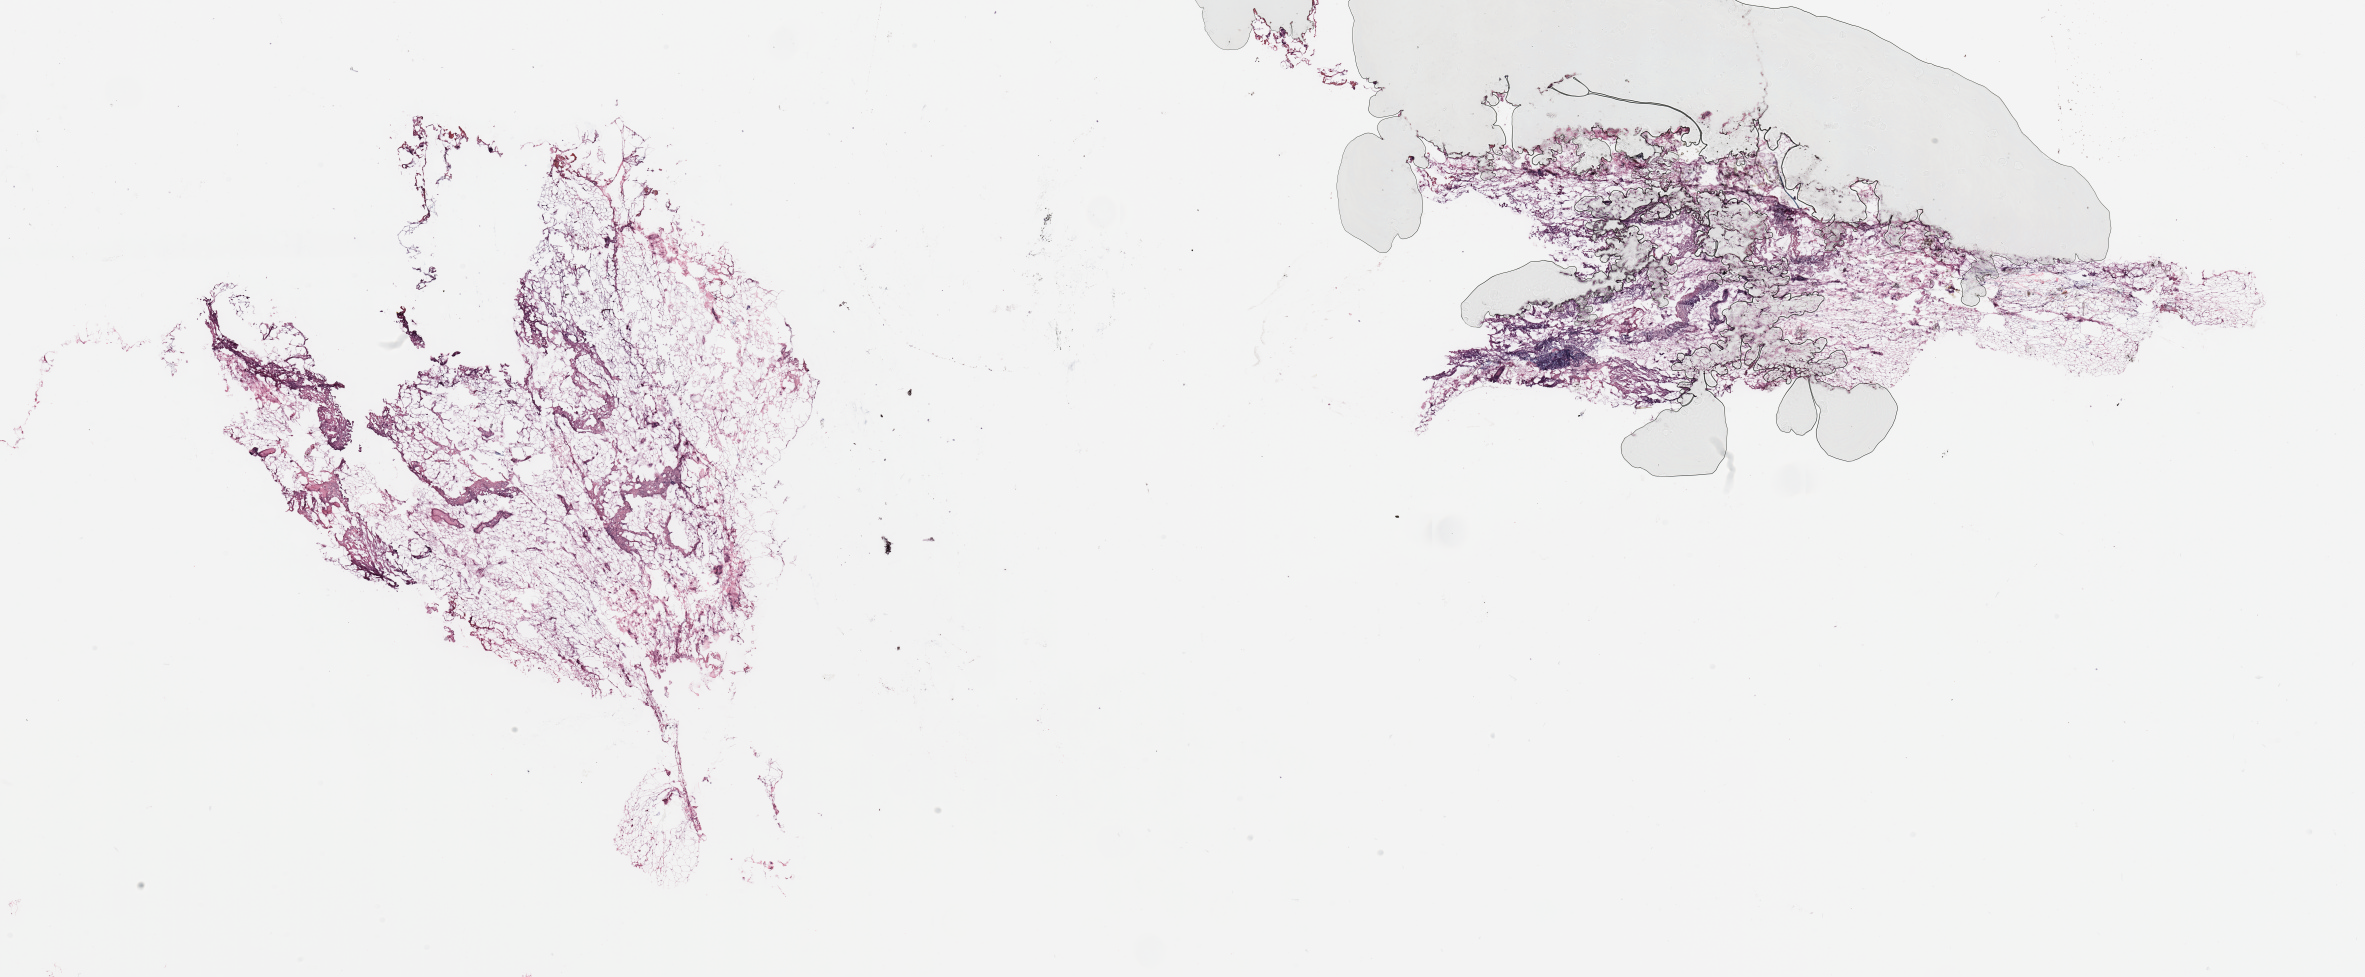
Digitized H&E tissue section (whole slide), low-resolution overview of the scanned area, about 37.4 x 15.5 mm. Breast, tumour tissue. 66-year-old female patient.
AJCC pathologic stage: IIIA. Diagnosis: Infiltrating duct carcinoma, NOS.